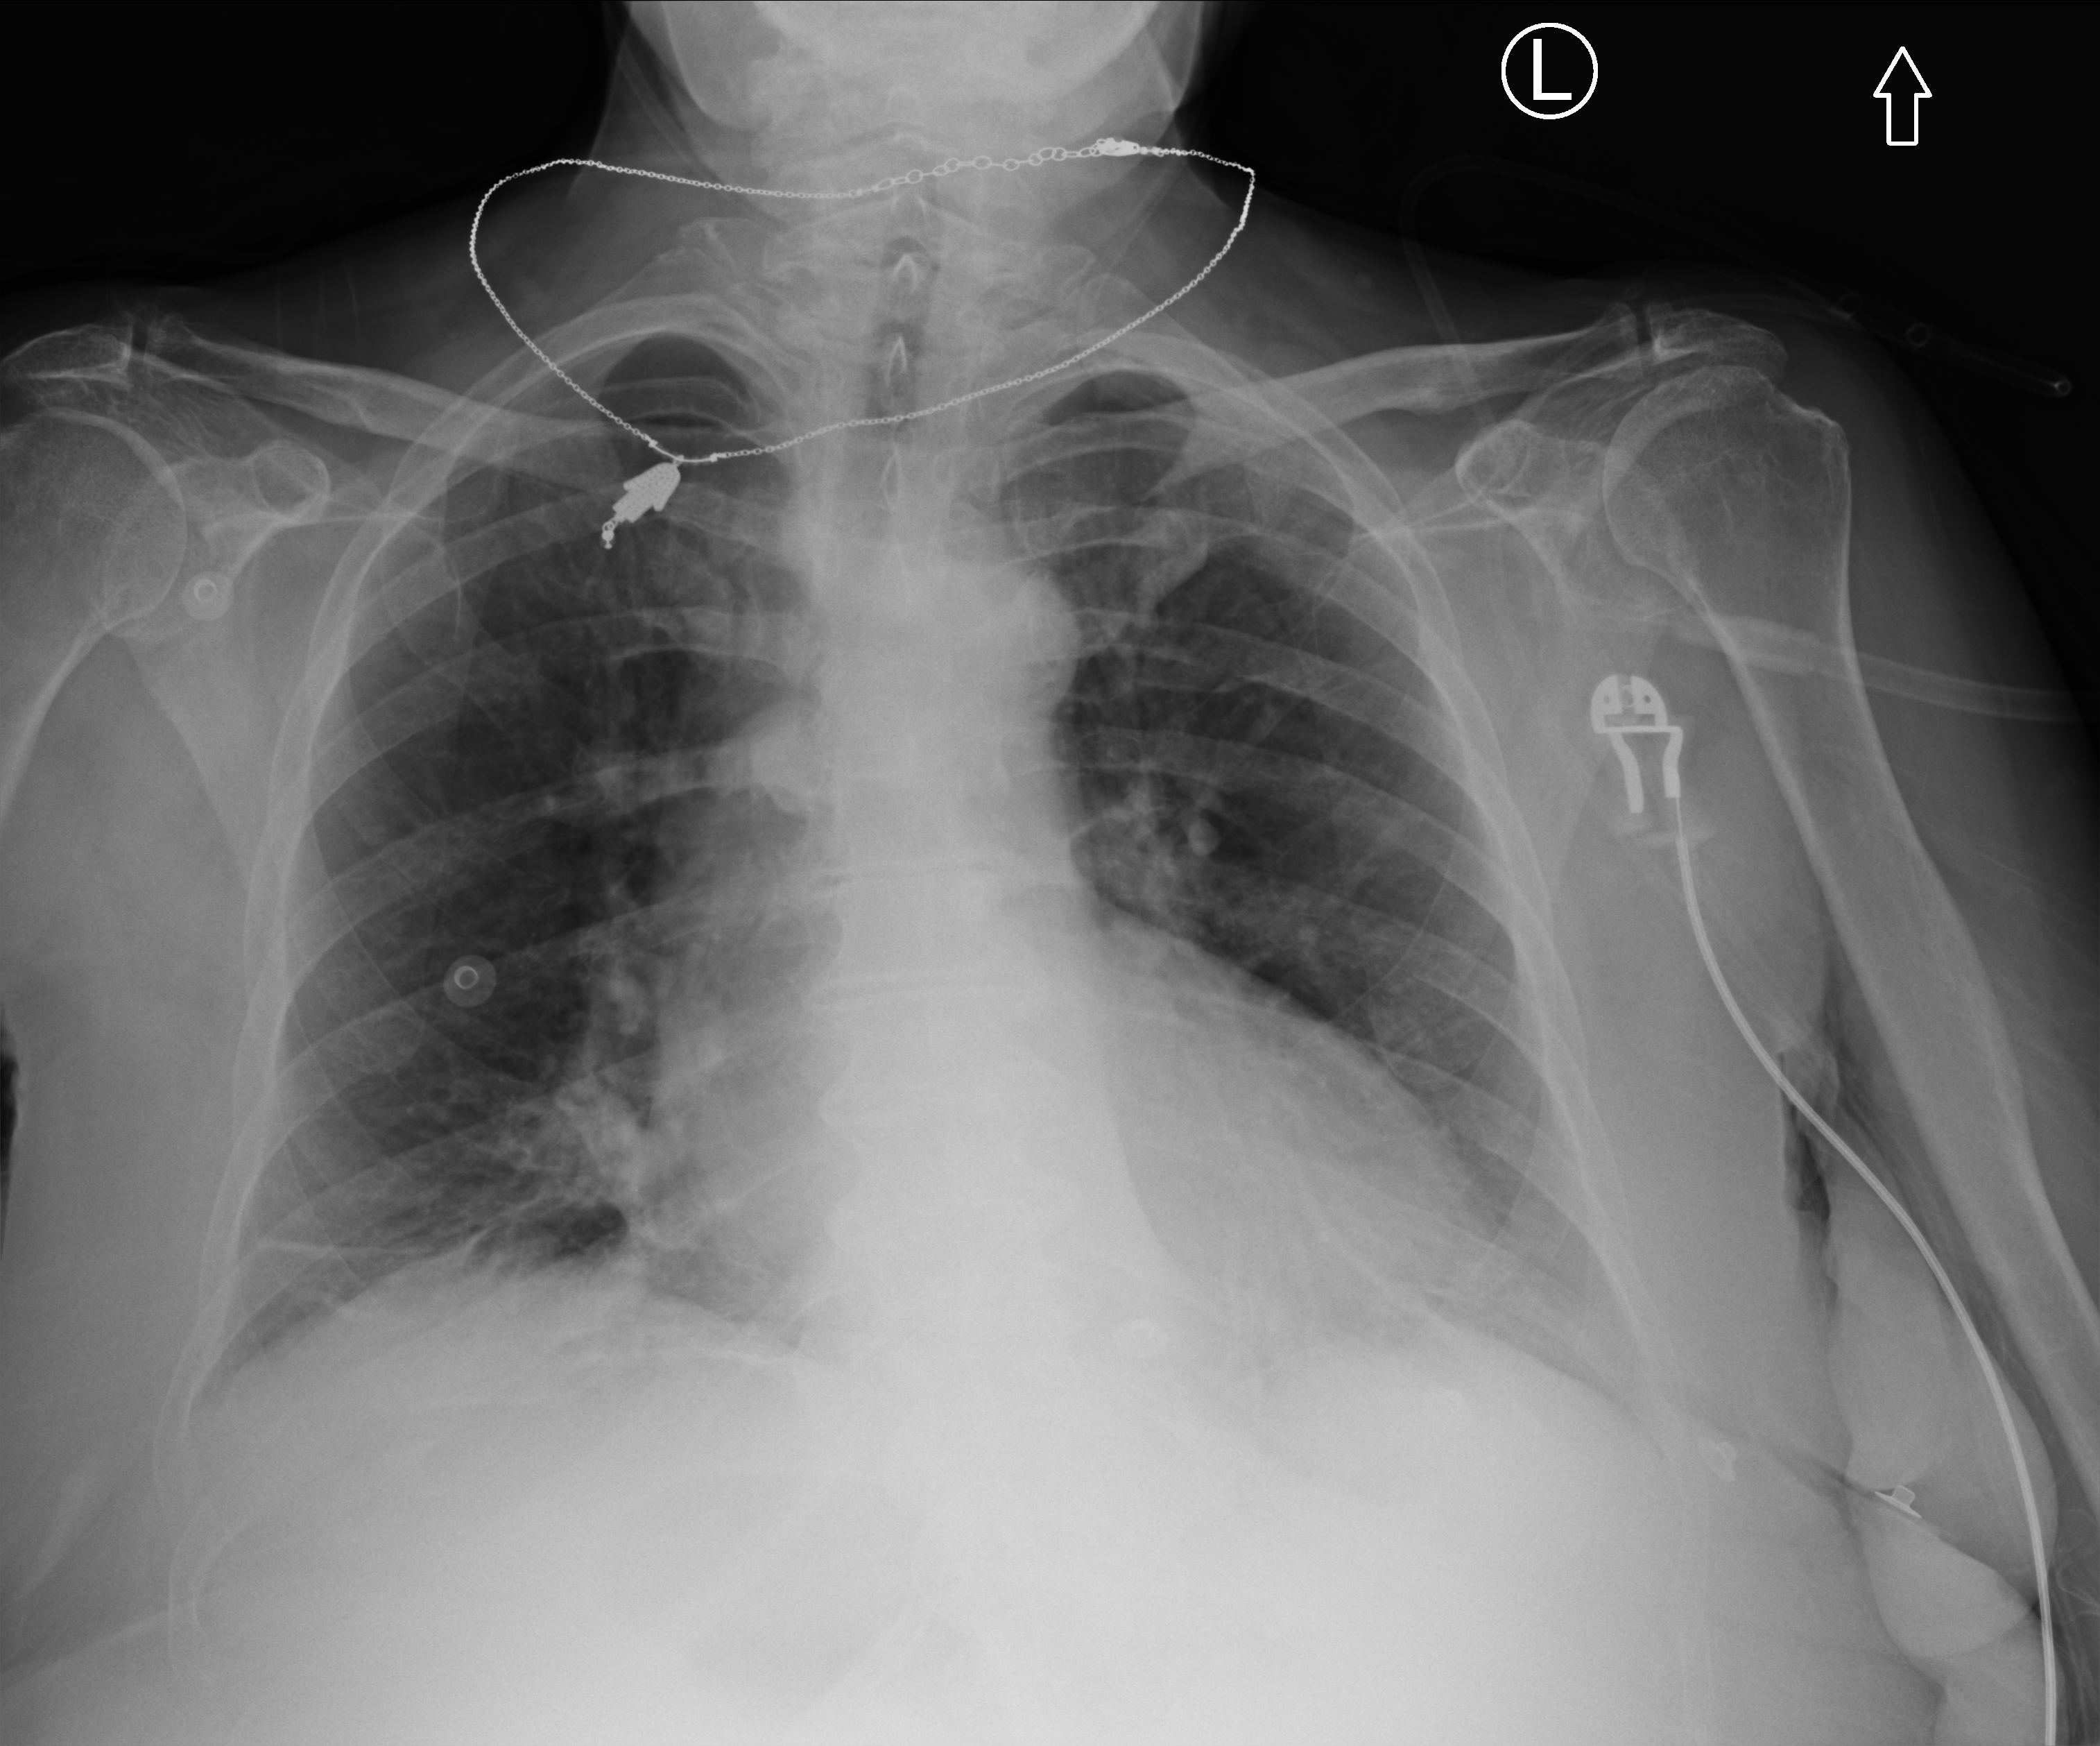
Bedside chest radiograph (computed radiography), anteroposterior (AP) projection. Female patient hospitalised with COVID-19, age 60–74 years.
Hospital-stay facts (about this admission, not read from this image; timing relative to this image not recorded):
- mechanically ventilated during this hospital stay: no